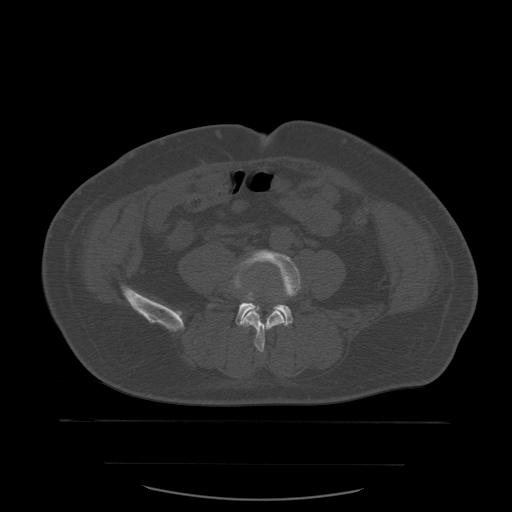
CT including the spine, one axial slice; slice 153 of 590 in the series (ordered by position); bone window (W 1800 / L 400 HU); 512 × 512 image matrix, field of view 479 × 479 mm. Patient age 71 years. Case-level facts recorded for this patient, not image findings: primary cancer: lung; vertebrae with lytic lesions (as recorded): T1, T2, L5, S1.
Outlined on this slice (semi-automatic segmentation, software-assisted and operator-edited):
- L4 vertebra: box from (x=233, y=250) to (x=301, y=353) px
- L5 vertebra: (x=209, y=287)–(x=293, y=327)